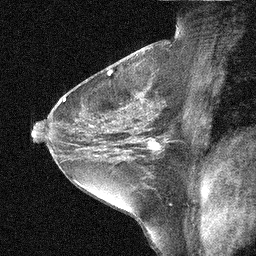
Breast MRI (dynamic contrast-enhanced), one sagittal slice; slice 25 of 44 in the series (ordered by position); dynamic contrast-enhanced study with each time point stored as its own series, time point 2 of 3 at this slice position (early post-contrast, ordered by acquisition time); 1.5 T; TE 5 ms, TR 10.3 ms; 3 mm slice thickness; 256 × 256 image matrix. Female patient, age 31 years. Case-level facts recorded for this patient, not image findings: setting: breast cancer imaged before/during neoadjuvant chemotherapy; receptor status: HER2-positive.
Structures marked on this image (semi-automatic segmentation, software-assisted and operator-edited):
- analysis volume of interest (the breast-tissue region the enhancement analysis was run in; not a lesion): bounding box [x1, y1, x2, y2] px = [136, 131, 181, 168]
- tumour enhancement mask (voxels above the 90 % enhancement threshold inside the analysis volume of interest): [138, 139, 168, 155]